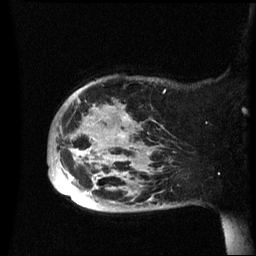
Breast MRI (dynamic contrast-enhanced), one sagittal slice. Position 11 of 60 along the scan axis. Dynamic contrast-enhanced series, image 2 of 3 at this slice position (ordered by acquisition). 1.5 T. TE 4.2 ms, TR 8.4 ms. 2.4 mm slice thickness. 256 × 256 image matrix, field of view 230 × 230 mm. Patient: female, 49 years.
Annotated regions visible in this slice (semi-automatic segmentation, software-assisted and operator-edited):
- analysis volume of interest (the breast-tissue region the enhancement analysis was run in; not a lesion): bounding box (x1, y1, x2, y2) in pixels: (48, 76, 174, 212)
- tumour enhancement mask (voxels above the 70 % enhancement threshold inside the analysis volume of interest): (60, 176, 72, 193)